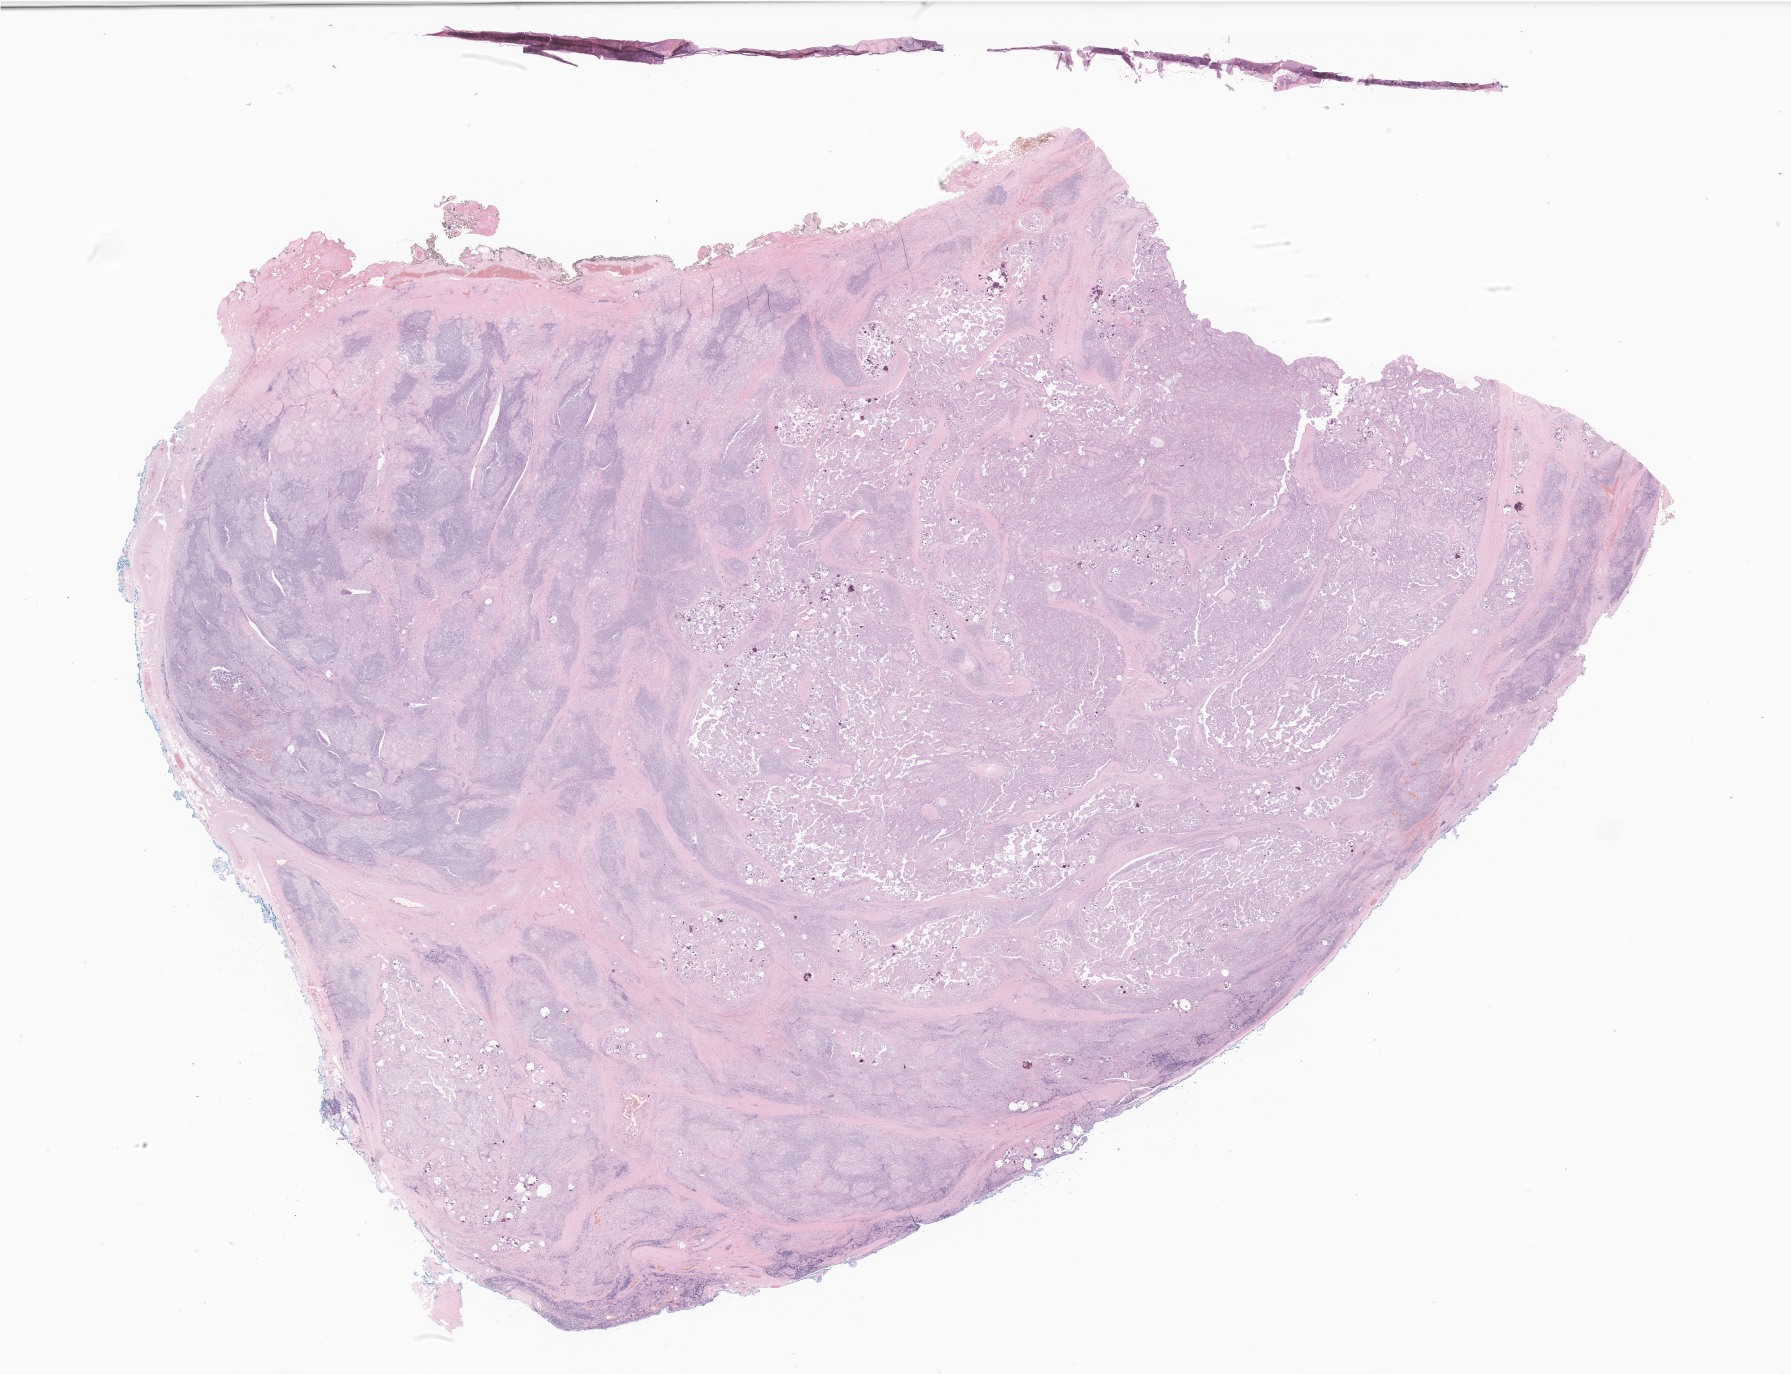
Whole-slide image, H&E stain of tumor tissue from the thyroid, low-resolution overview of the scanned area, about 30.2 x 23.2 mm; formalin-fixed paraffin-embedded section. Patient: female, age 203 months (16 years 11 months).
Diagnosis (ICD-O-3 morphology term): Papillary carcinoma, NOS.